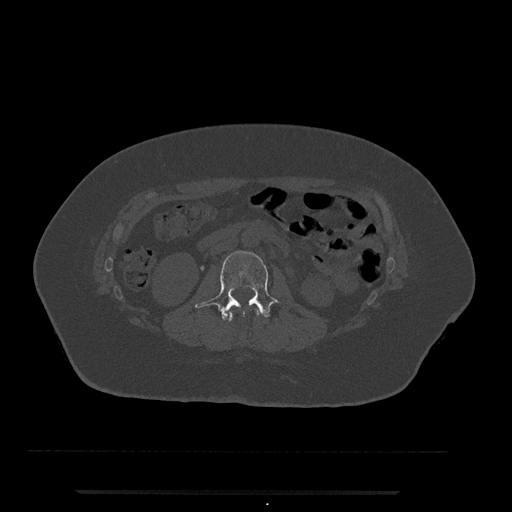
CT including the spine, one axial slice; slice 42 of 797 in the series (ordered by position); reconstruction kernel Br40s/3; 120 kVp; bone window (W 1800 / L 400 HU); 0.5 mm slice thickness; 512 × 512 image matrix. Female patient, age 51 years. Case-level facts recorded for this patient, not image findings: primary cancer: neuro; vertebrae with lytic lesions (as recorded): T8.
Outlined on this slice (semi-automatic segmentation, software-assisted and operator-edited):
- L1 vertebra: bounding box [x1, y1, x2, y2] px = [227, 309, 262, 322]
- L2 vertebra: [195, 251, 281, 321]